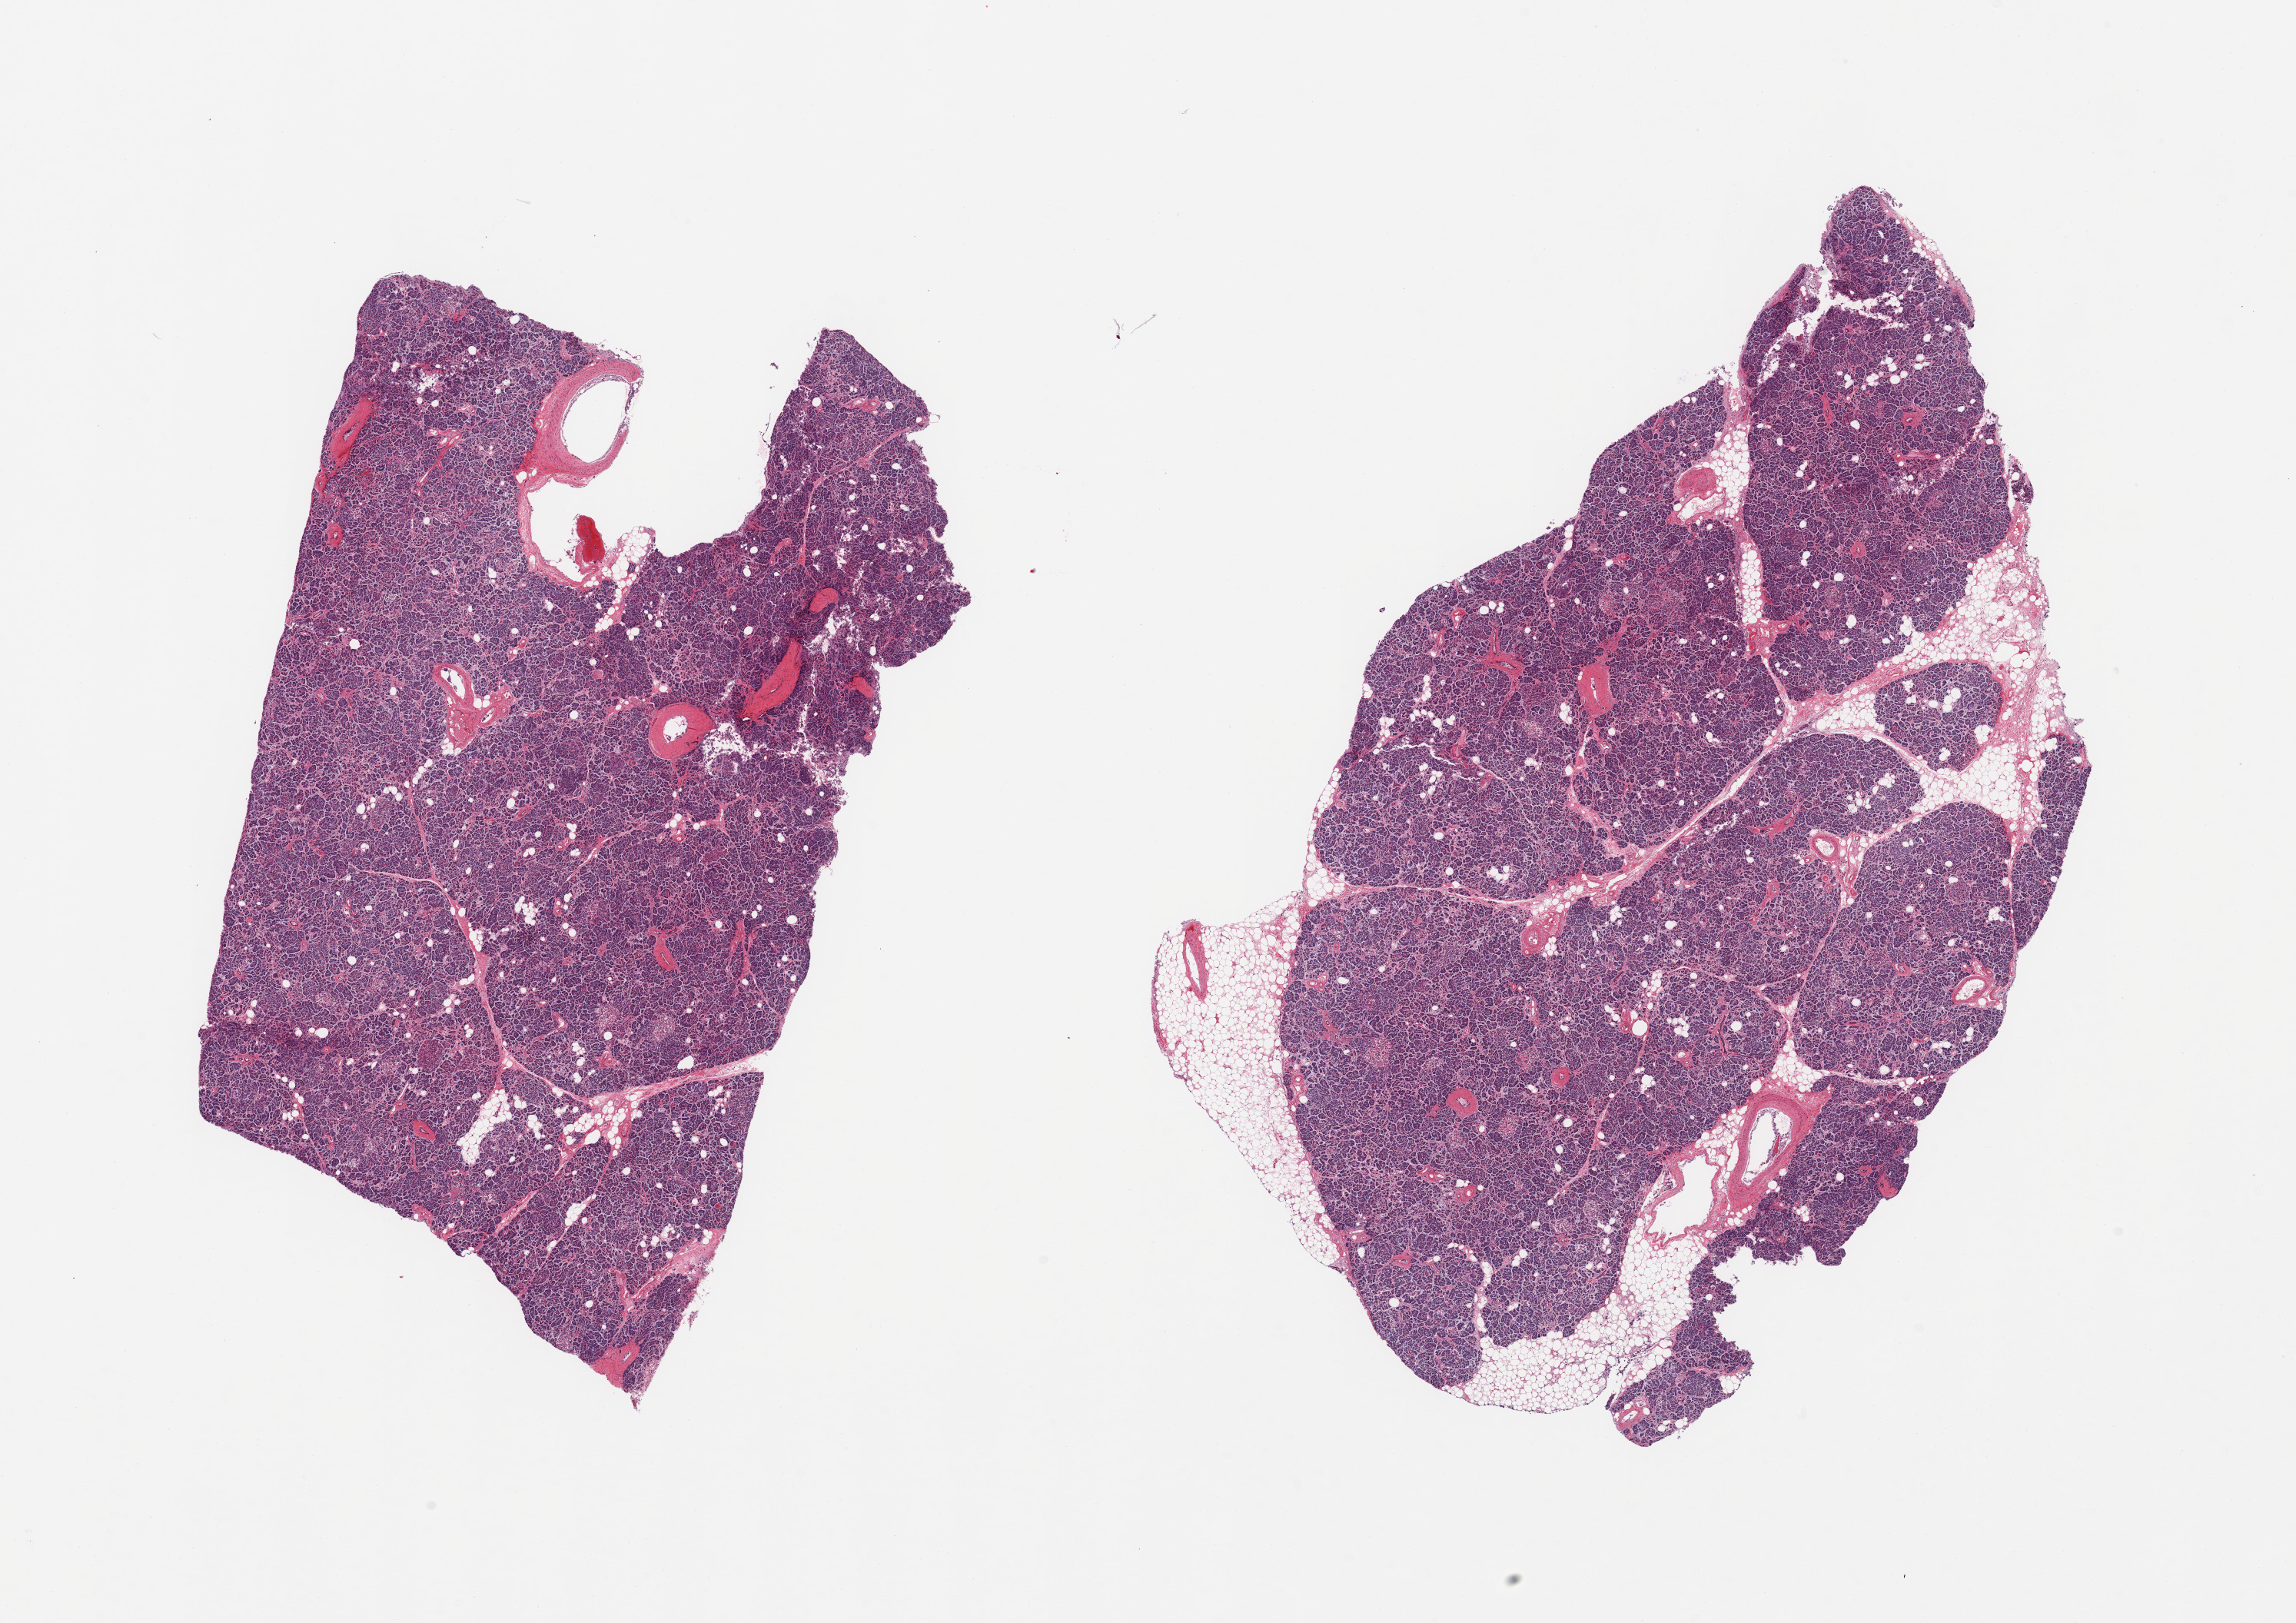
Digitized haematoxylin and eosin-stained section — shown as a low-resolution overview of the whole scanned area (about 23.6 x 16.7 mm). PAXgene-fixed paraffin-embedded (PFPE) section. Section of pancreas (target tissue). Donor tissue sample. Donor: male.
- pathologist's review note for this sample: 2 pieces, moderately advanced saponification; Islets still visible but markedly autolyzed